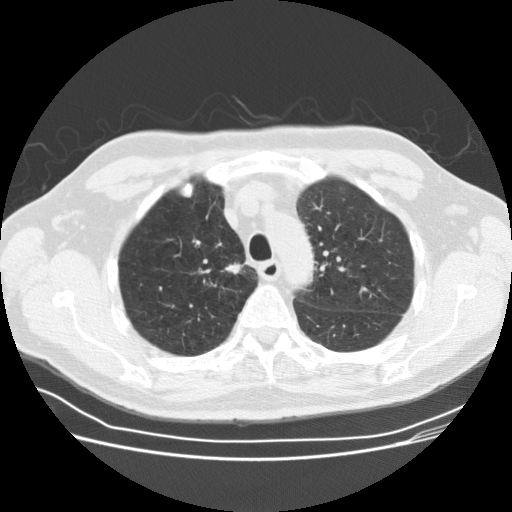
Low-dose screening chest CT, one axial slice; lung window (W 1500 / L -600 HU); 2.5 mm slice thickness; 512 × 512 image matrix, field of view 360 × 360 mm.
Outlined on this slice (expert manual segmentation):
- lesion 1 (tumor, upper lobe of right lung): box from (x=225, y=263) to (x=244, y=275) px